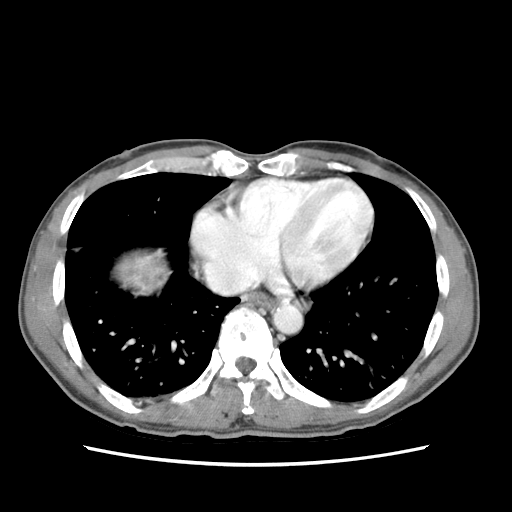
Contrast-enhanced abdominal CT (liver protocol), one axial slice. Slice 73 of 79 in the series (ordered by position). Reconstruction kernel STANDARD. 120 kVp. Soft-tissue window (W 400 / L 40 HU). 512 × 512 image matrix, field of view 320 × 320 mm. From the clinical record (not read from this slice): diagnosis: hepatocellular carcinoma (patient treated with transarterial chemoembolisation; whether this scan precedes or follows treatment is not stated here); TNM stage (as recorded): Stage-IIIB; Child-Pugh class: A; tumour differentiation: moderately differentiated.
Outlined on this slice (semi-automatic segmentation, software-assisted and operator-edited):
- liver parenchyma outside the tumour (the mass and vessels are separate outlines, so this box may not span the whole liver): bounding box (x1, y1, x2, y2) in pixels: (145, 293, 154, 296)
- mass: (111, 238, 175, 296)